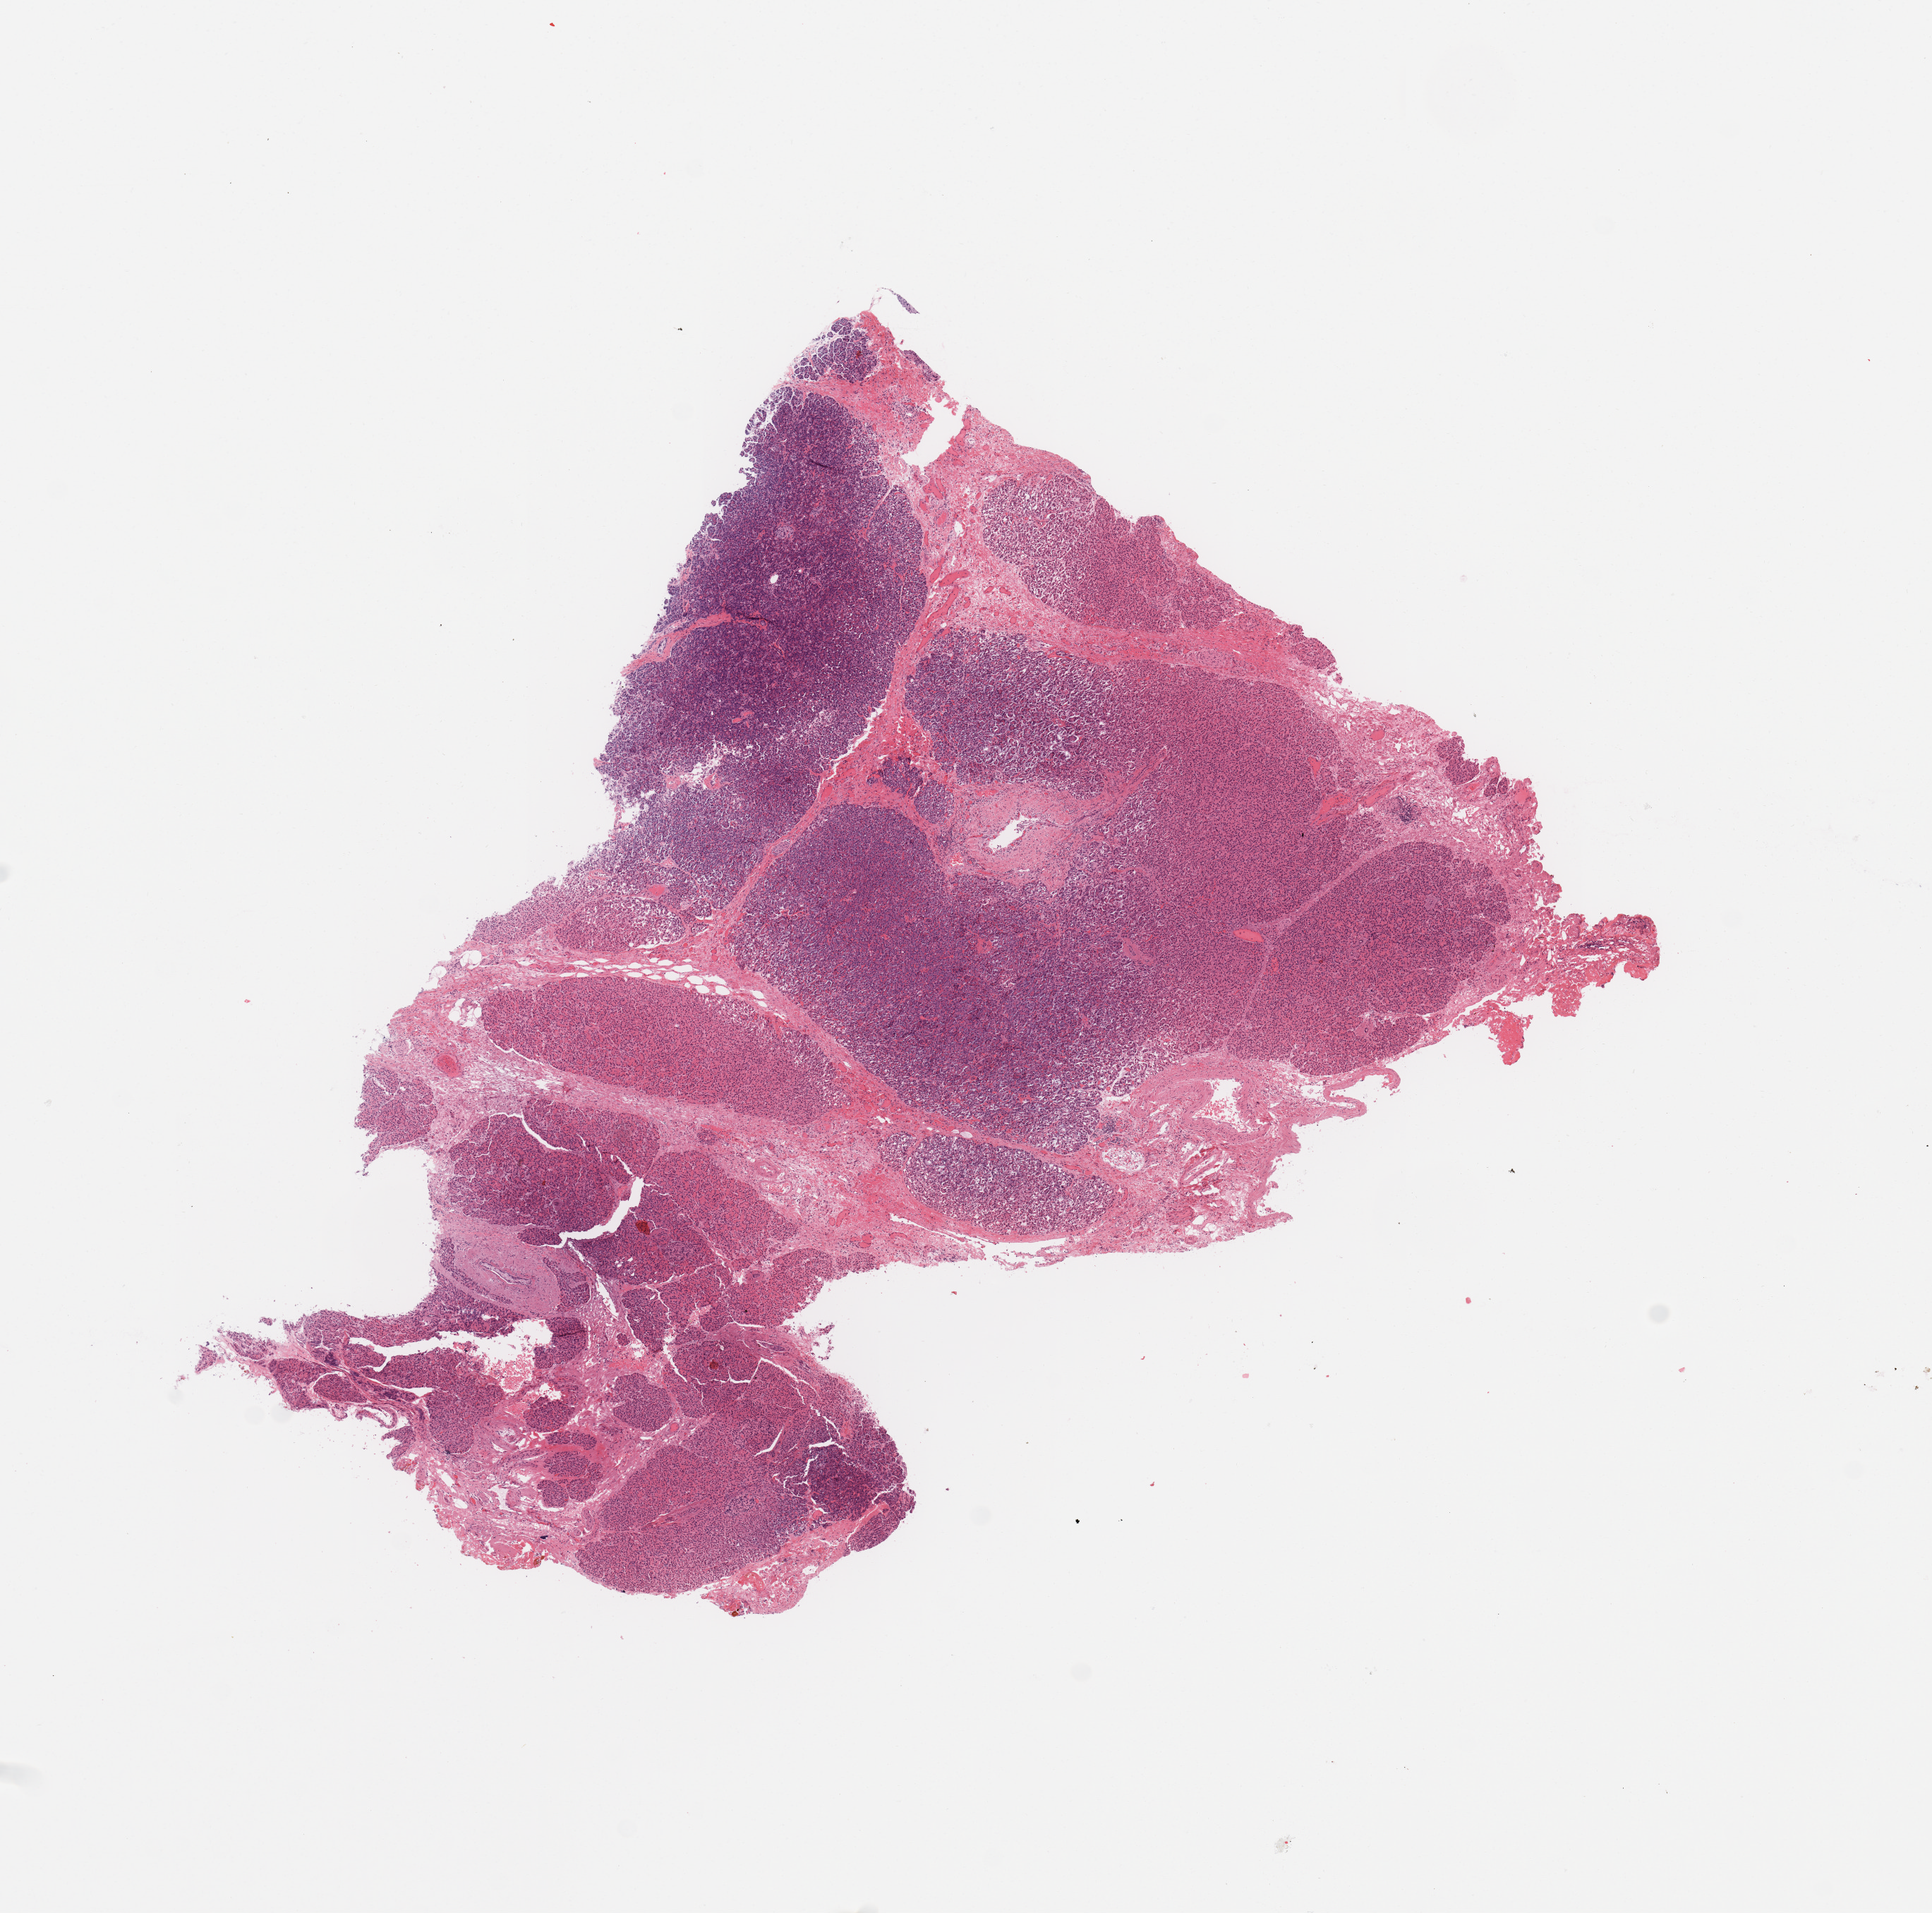
H&E whole-slide image — whole scanned area (about 10.8 x 10.7 mm) shown as a low-resolution overview, normal (non-tumour) tissue sample, sampled site: pancreas. 50-year-old female patient.
This section: normal (non-tumour) tissue from the same patient. Patient diagnosis: Infiltrating duct carcinoma, NOS.